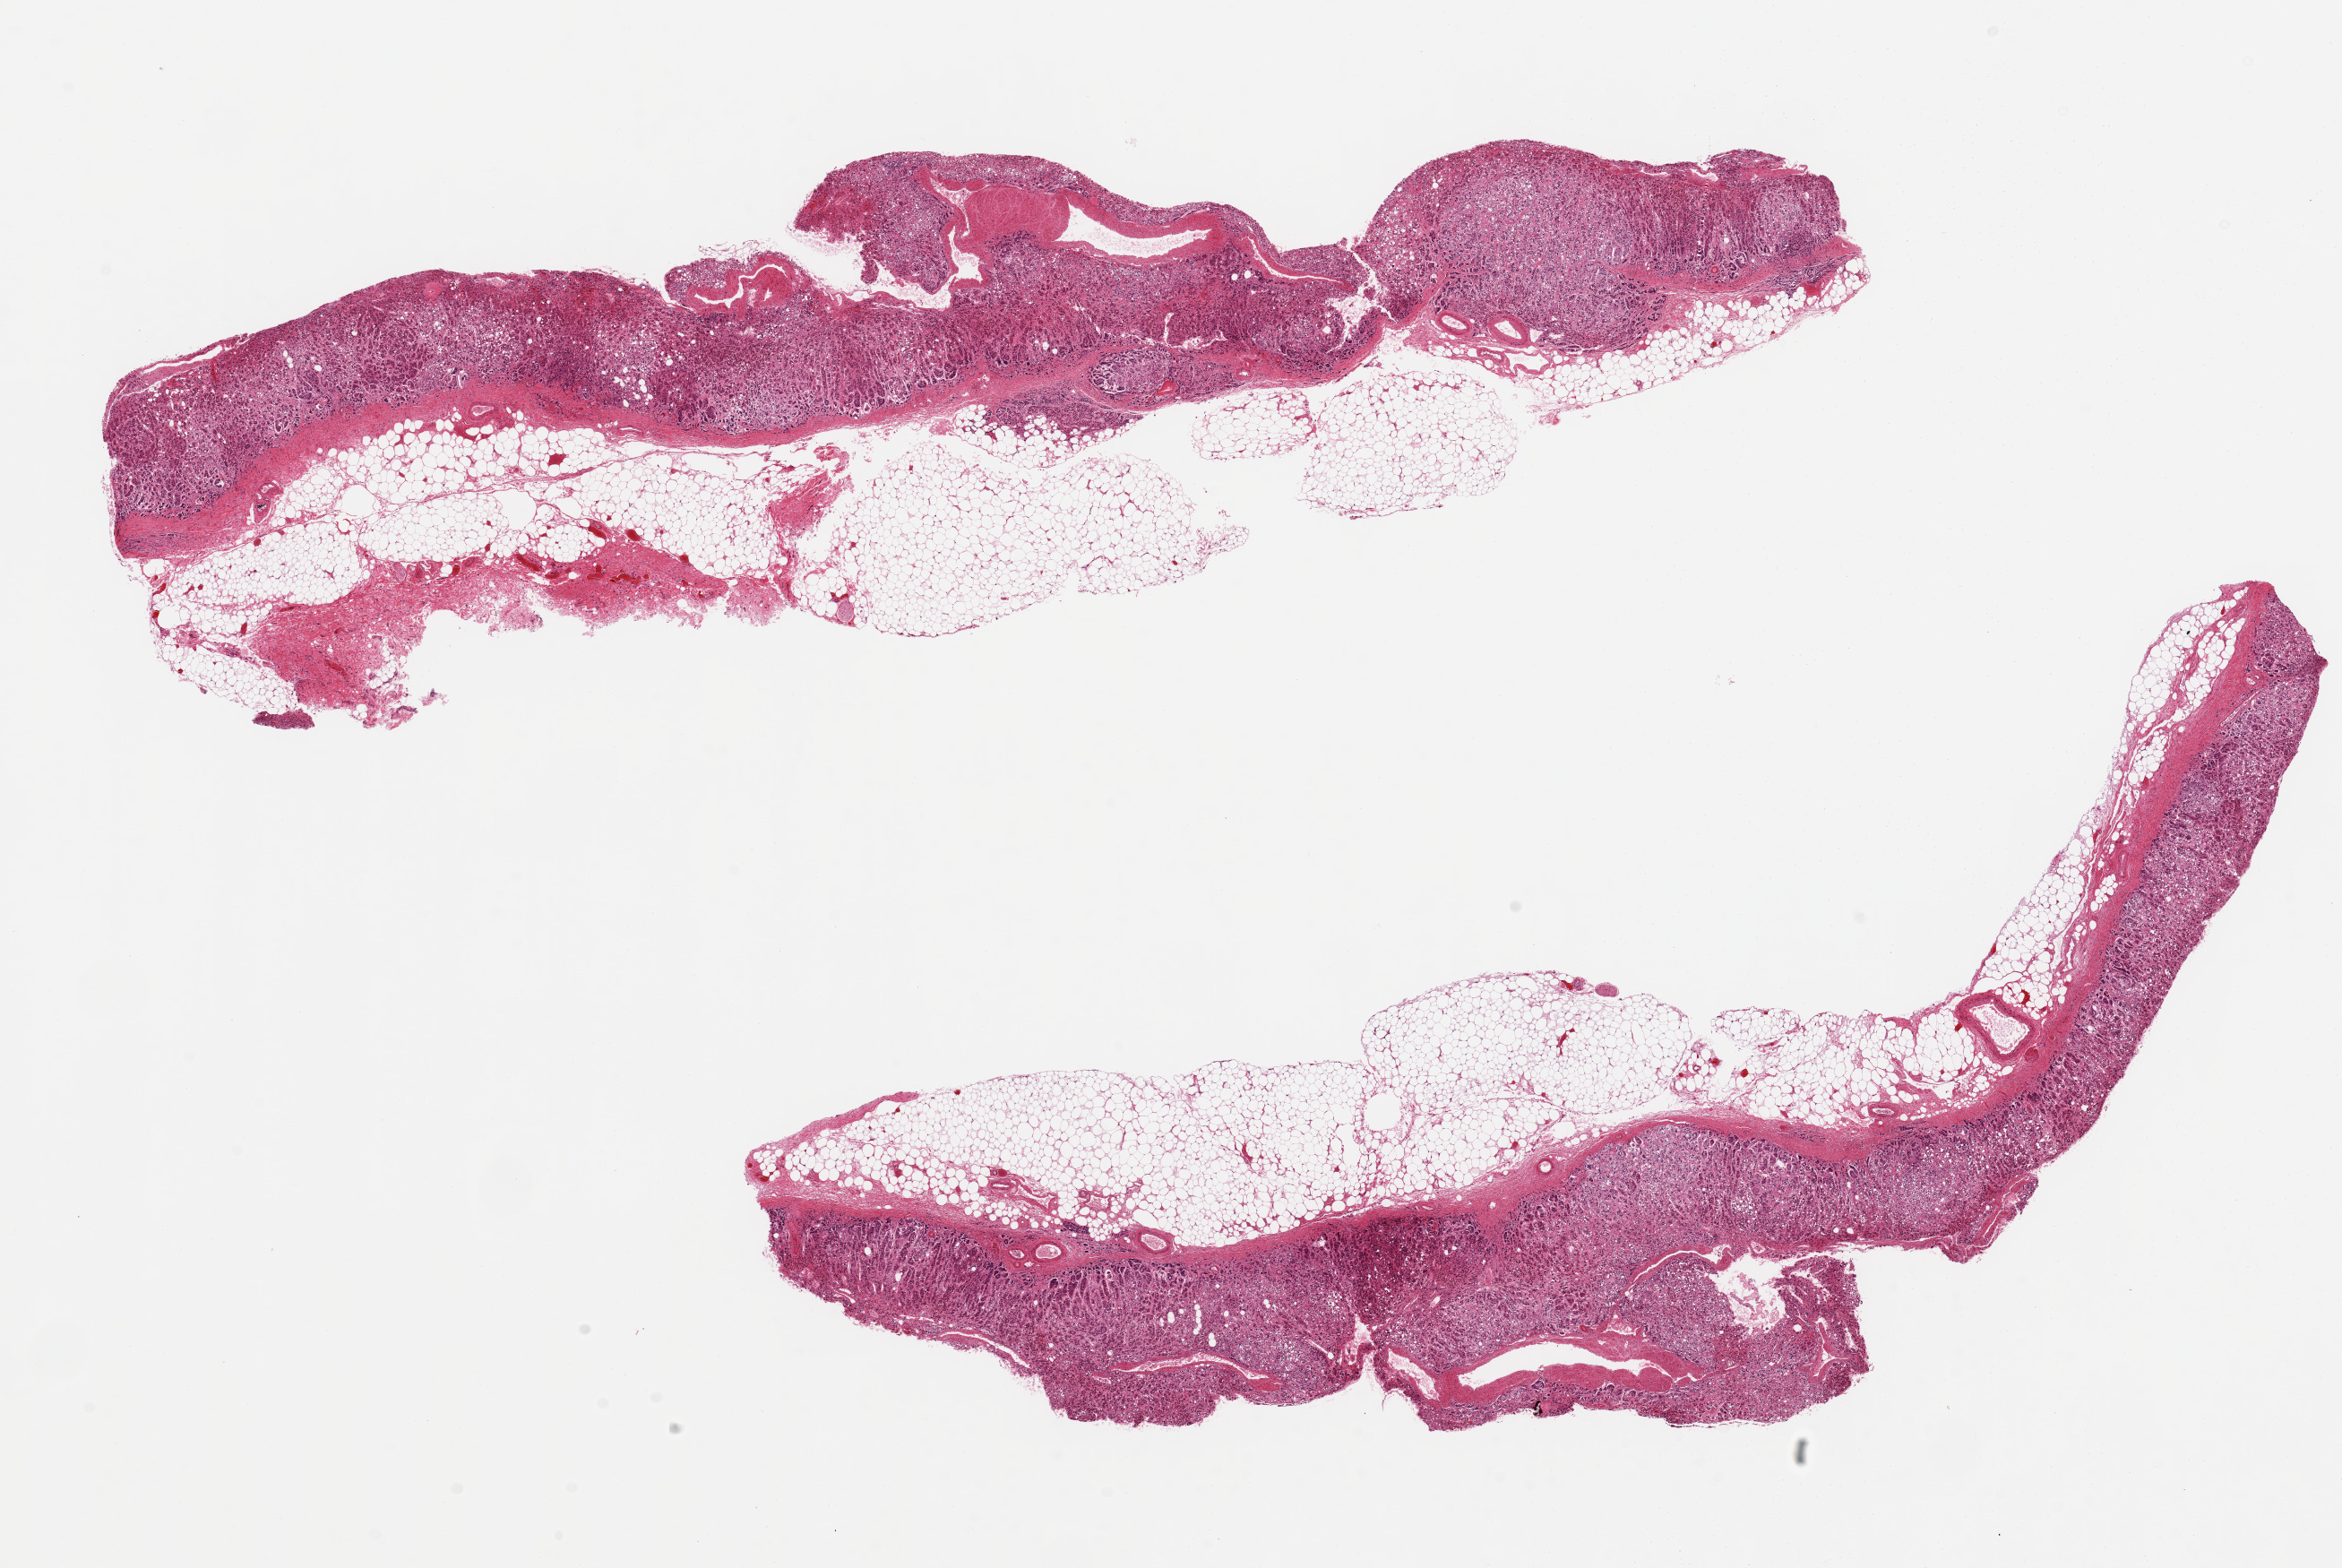
Hematoxylin and eosin (H&E) whole-slide image, brightfield, low-resolution overview of the scanned area, about 20.7 x 13.8 mm (from a 20x scan), PAXgene-fixed, paraffin-embedded tissue, section of adrenal gland (target tissue), tissue donor sample. Male donor.
Review note (as recorded): 2 aliquots, ~15x3.5mm. ~50% of each is adherent fat.